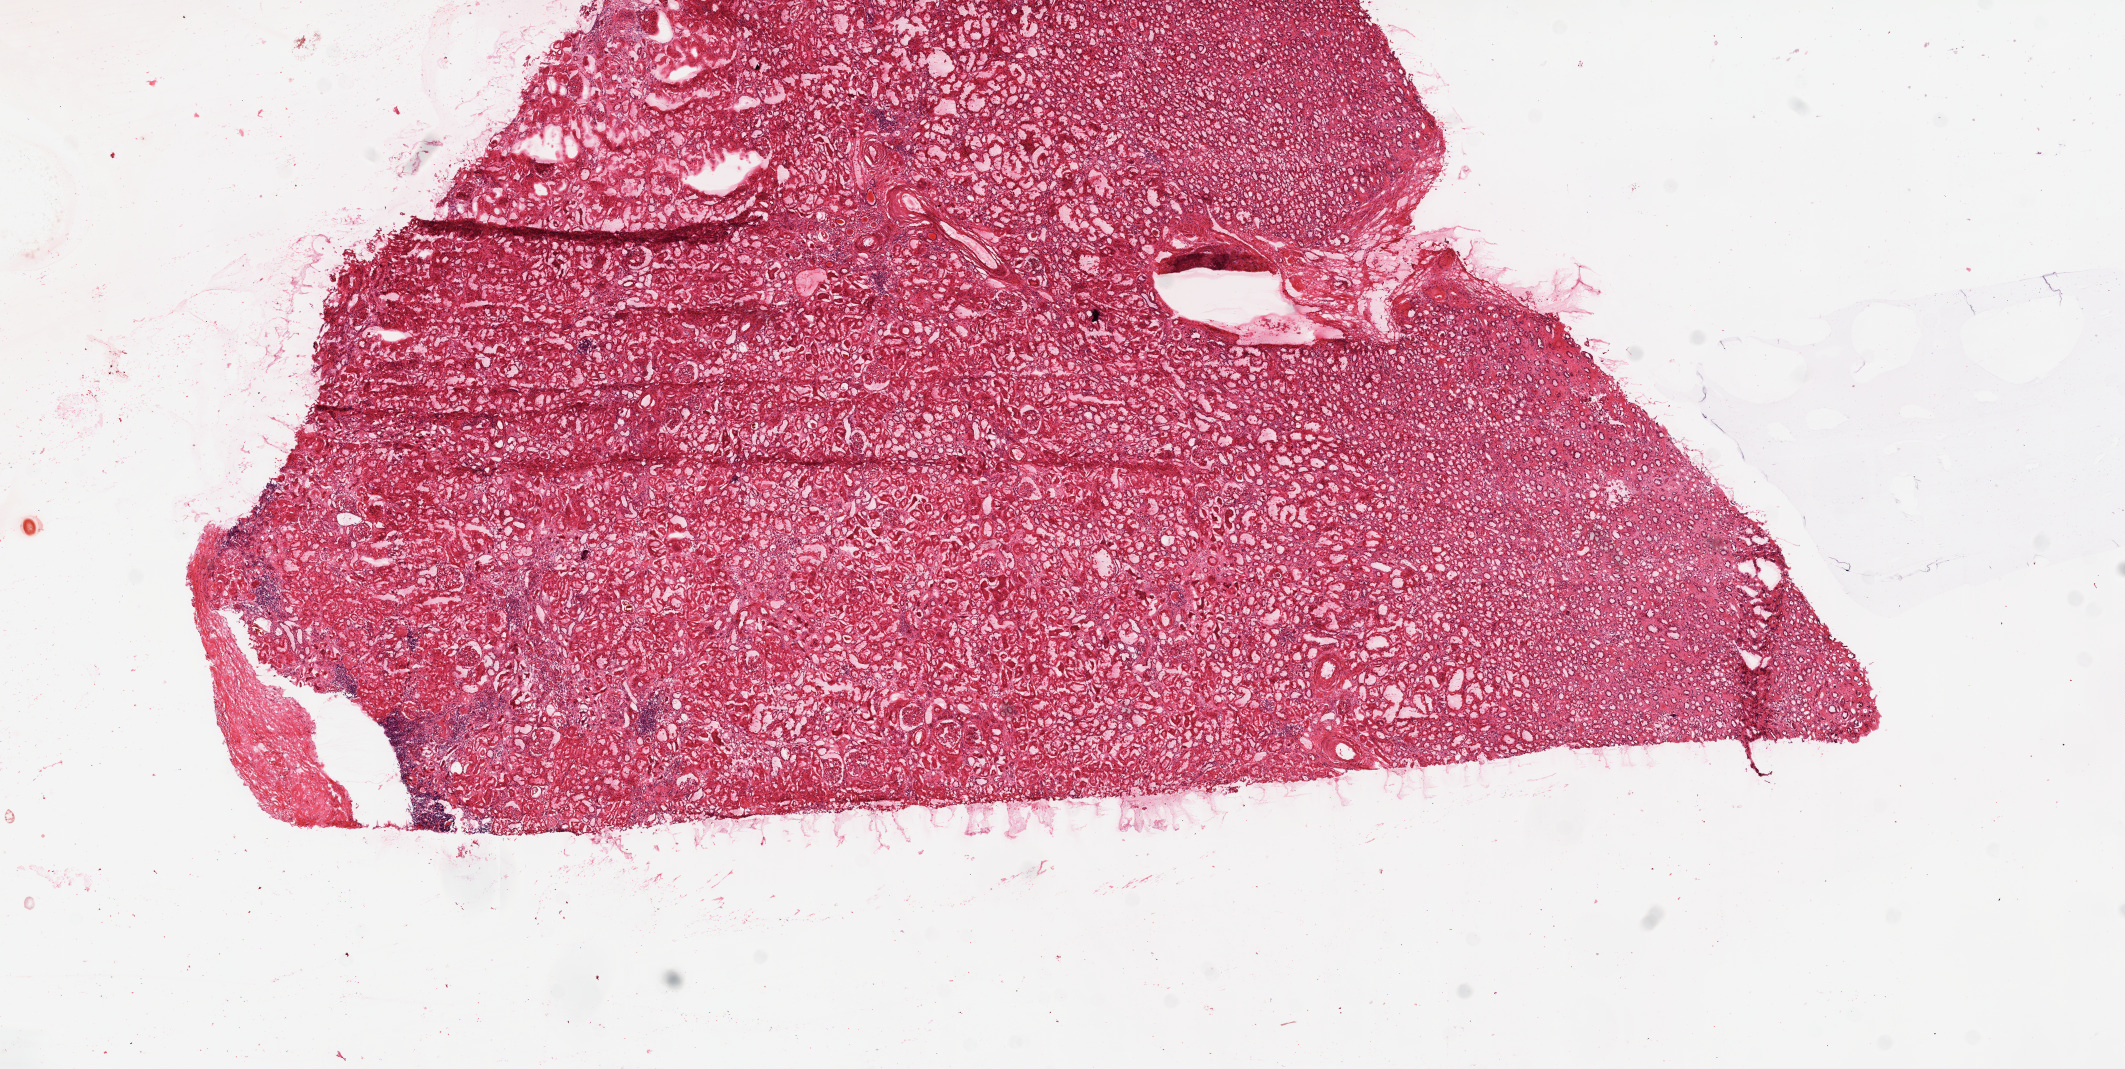
Digitized H&E tissue section (whole slide) — low-resolution overview of the scanned area, about 17.1 x 8.6 mm (from a 20x scan). Frozen section from the top of the tissue portion. Kidney, solid tissue normal (non-tumour tissue) sample. Male, age 81 years at initial diagnosis.
* this section: solid tissue normal (non-tumour) sample from the same patient
* patient diagnosis: Clear cell adenocarcinoma, NOS